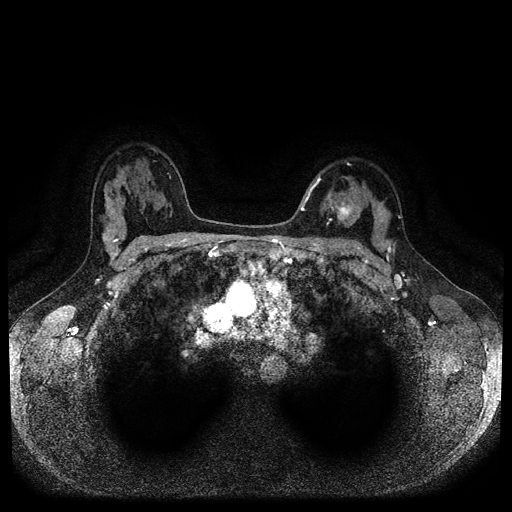
Breast MRI (dynamic contrast-enhanced, multi-phase), one axial slice. Slice 71 of 116 in the series (ordered by position). Dynamic contrast-enhanced series, time point 2 of 5 at this slice position (early post-contrast). 1.5 T. TE 2.6 ms, TR 5.3 ms. 2 mm slice thickness. 512 × 512 image matrix. Female patient, age 33 years.
Annotated regions visible in this slice (semi-automatic segmentation, software-assisted and operator-edited):
- breast lesion (labelled 'tumour' in the annotation; benign lesions carry a separate 'benign' label): bounding box [x1, y1, x2, y2] px = [334, 198, 356, 222]